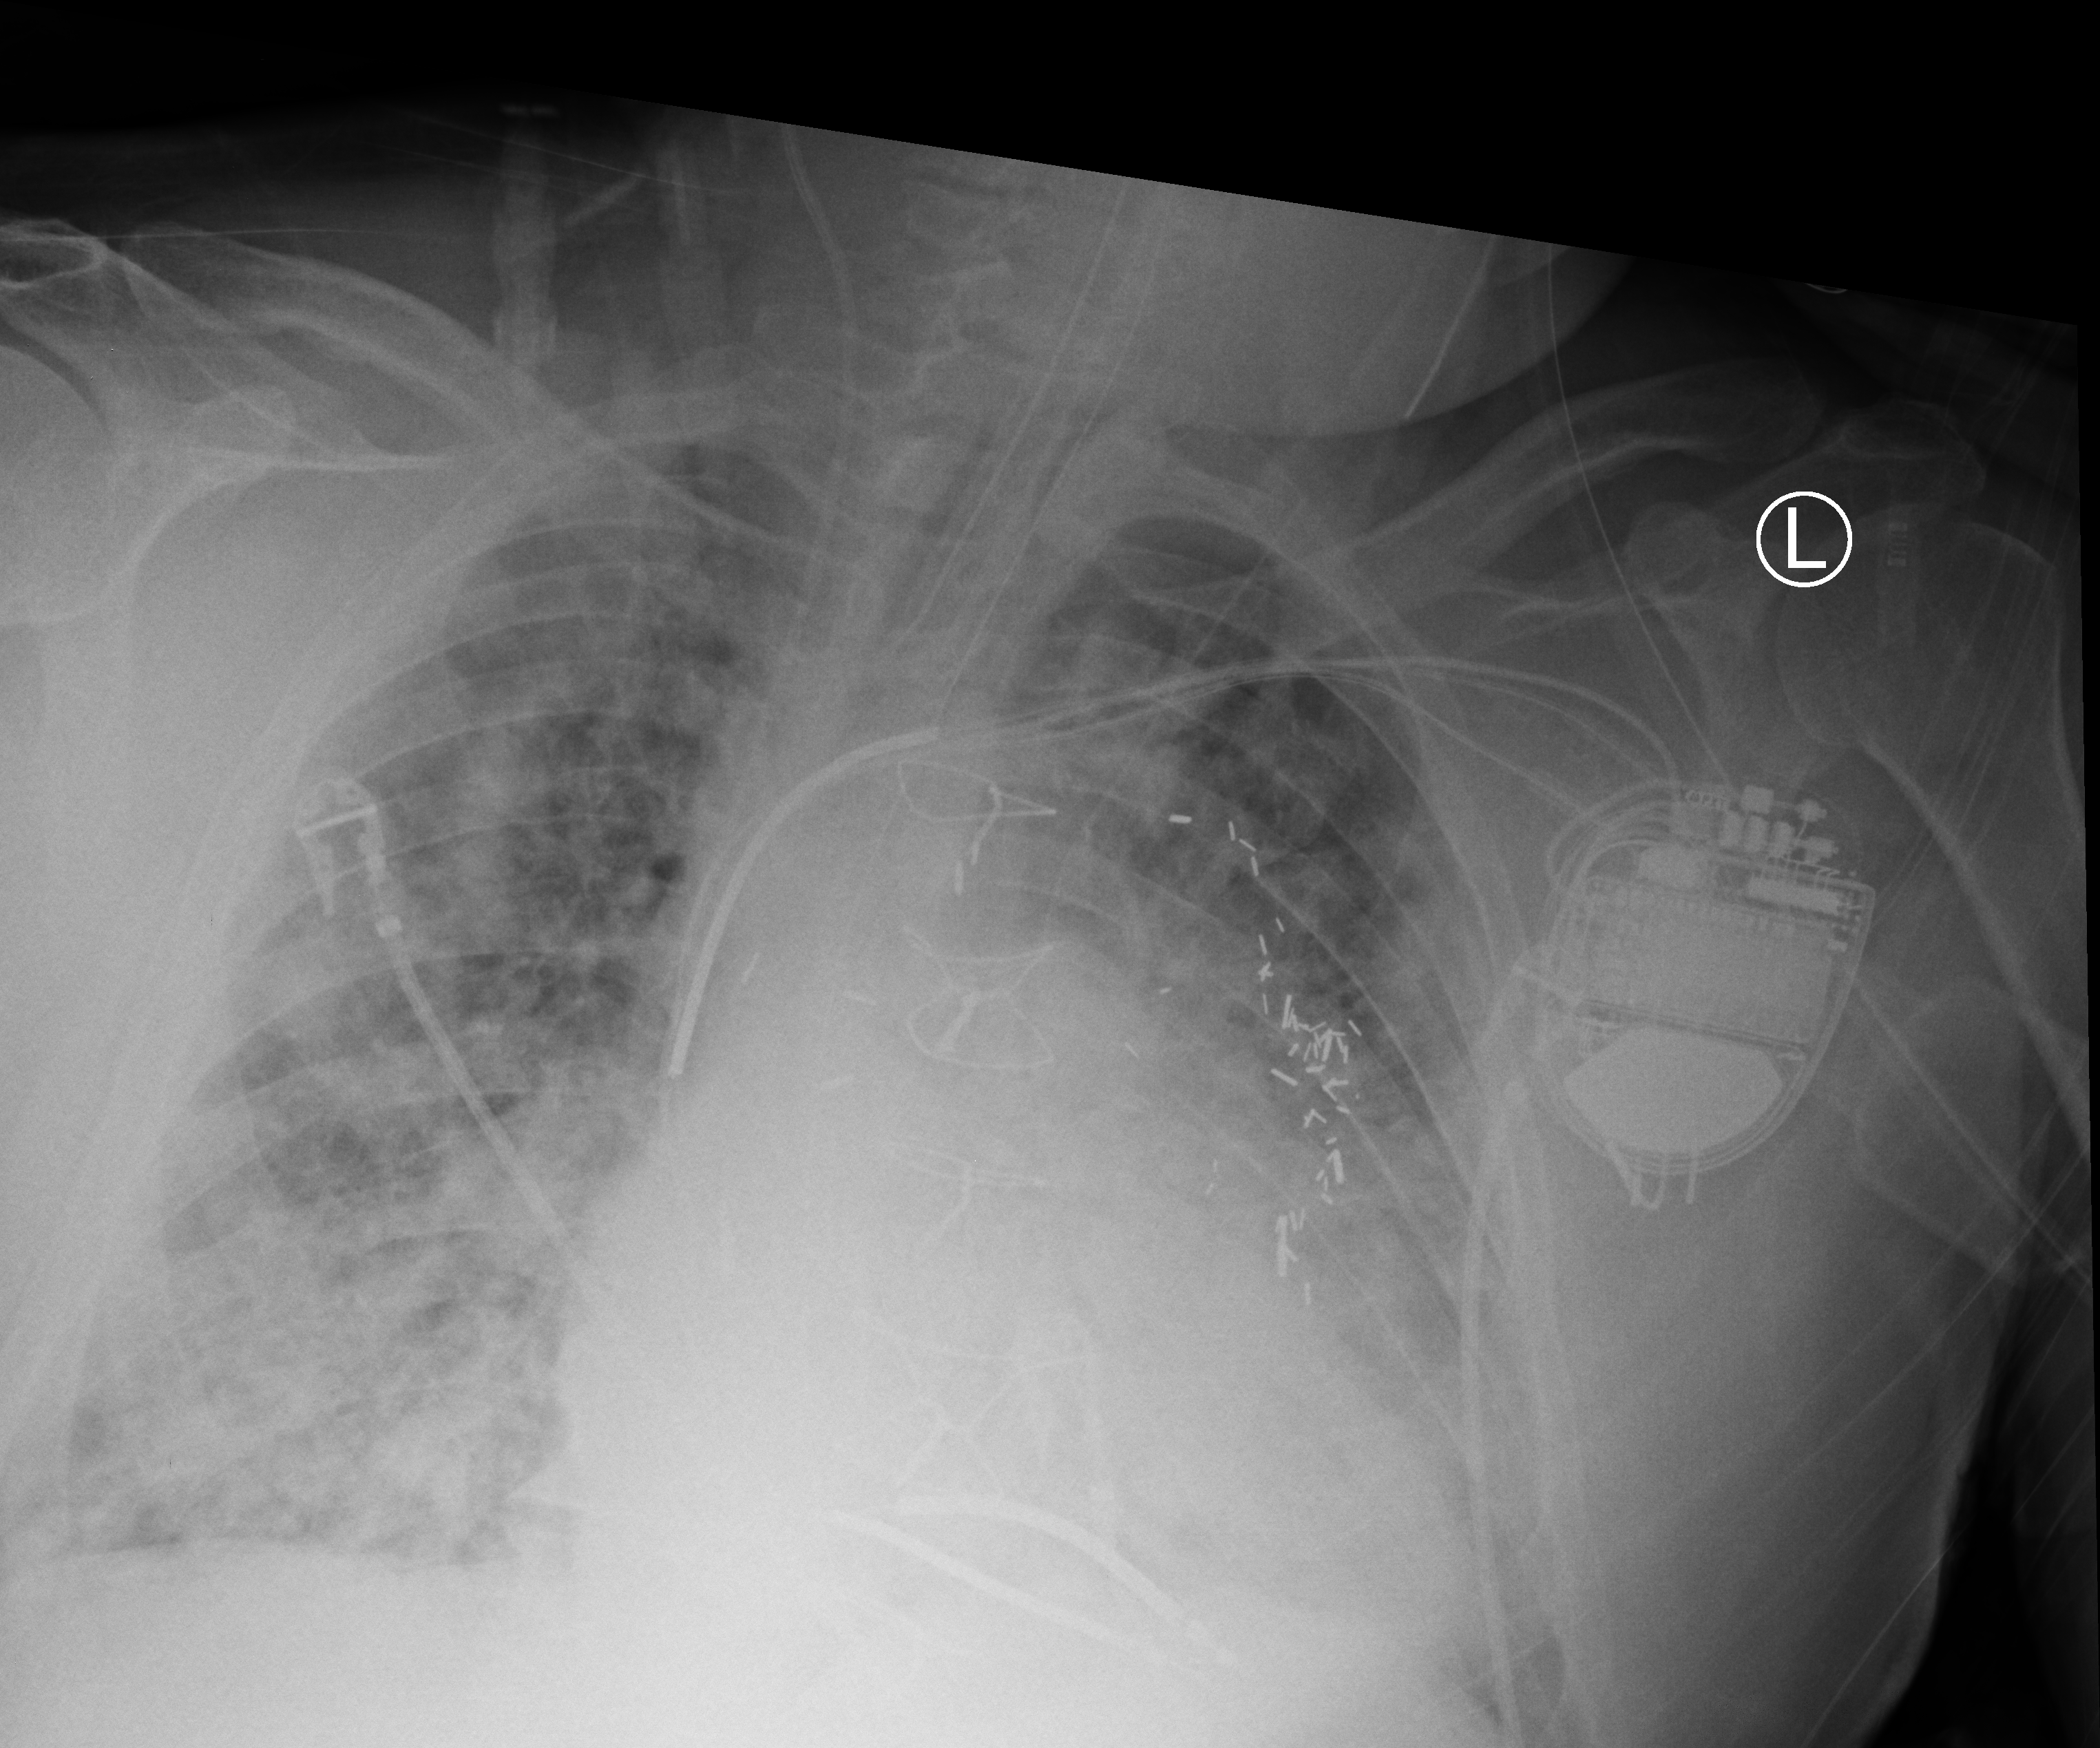
Chest X-ray (portable). Male patient hospitalised with COVID-19, age 60–74 years.
Hospital-stay facts (about this admission, not read from this image; timing relative to this image not recorded): admitted to intensive care during this hospital stay: yes; mechanically ventilated during this hospital stay: yes.